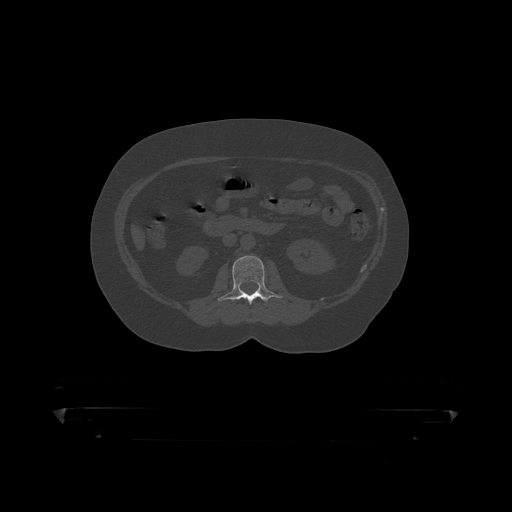
CT including the spine, one axial slice; slice 119 of 390 in the series (ordered by position); reconstruction kernel STANDARD; 120 kVp; bone window (W 1800 / L 400 HU); 512 × 512 image matrix. Patient: male, 60 years. From the clinical record (not read from this slice): primary cancer: prostate.
Outlined on this slice (semi-automatic segmentation, software-assisted and operator-edited):
- L2 vertebra: bounding box (x1, y1, x2, y2) in pixels: (218, 256, 283, 305)